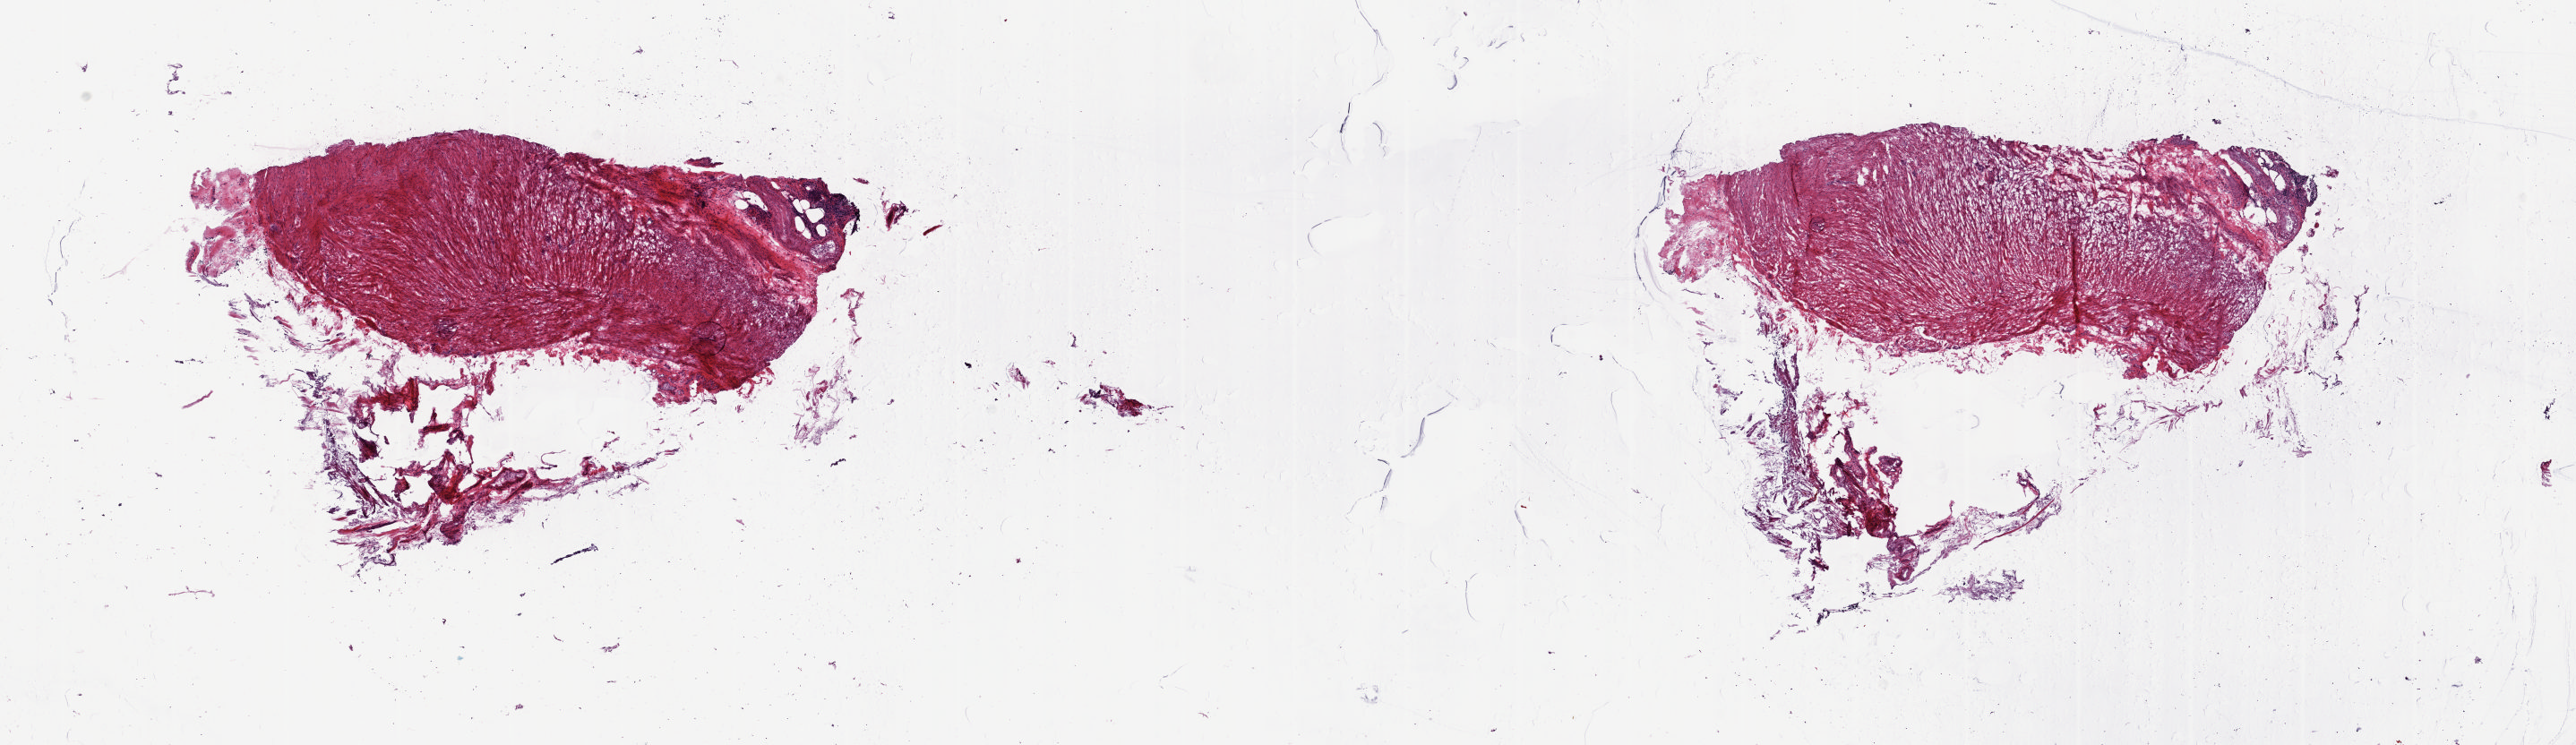
Whole-slide histology image, Hematoxylin and eosin (H&E) stained, shown as a low-resolution overview of the whole scanned area (about 22.8 x 6.6 mm, from a 20x scan). Frozen section from the top of the tissue portion. Sample: solid tissue normal (non-tumour tissue), uterus. Female, age 59 years at initial diagnosis.
This section: solid tissue normal (non-tumour) sample from the same patient. Patient diagnosis: Endometrioid adenocarcinoma, NOS (endometrium).